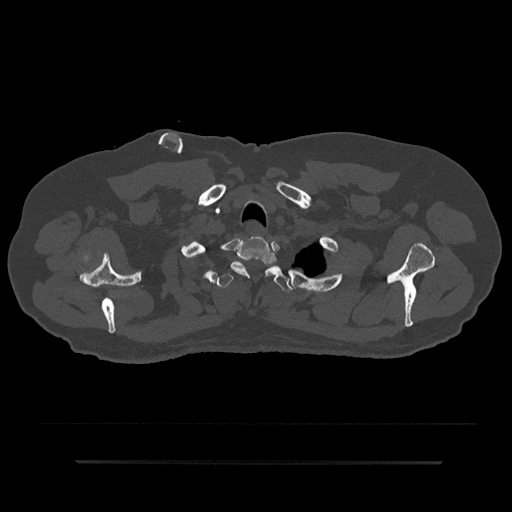
CT including the spine, one axial slice; slice 721 of 797 in the series (ordered by position); reconstruction kernel Br40s/3; bone window (W 1800 / L 400 HU); 0.5 mm slice thickness; 512 × 512 image matrix, field of view 464 × 464 mm. Male patient, age 59 years. From the clinical record (not read from this slice): primary cancer: bile ducts; vertebrae with lytic lesions (as recorded): T10.
Outlined on this slice (semi-automatically segmented with operator editing):
- T1 vertebra: bounding box [x1, y1, x2, y2] px = [230, 236, 278, 277]
- T2 vertebra: [214, 263, 292, 292]